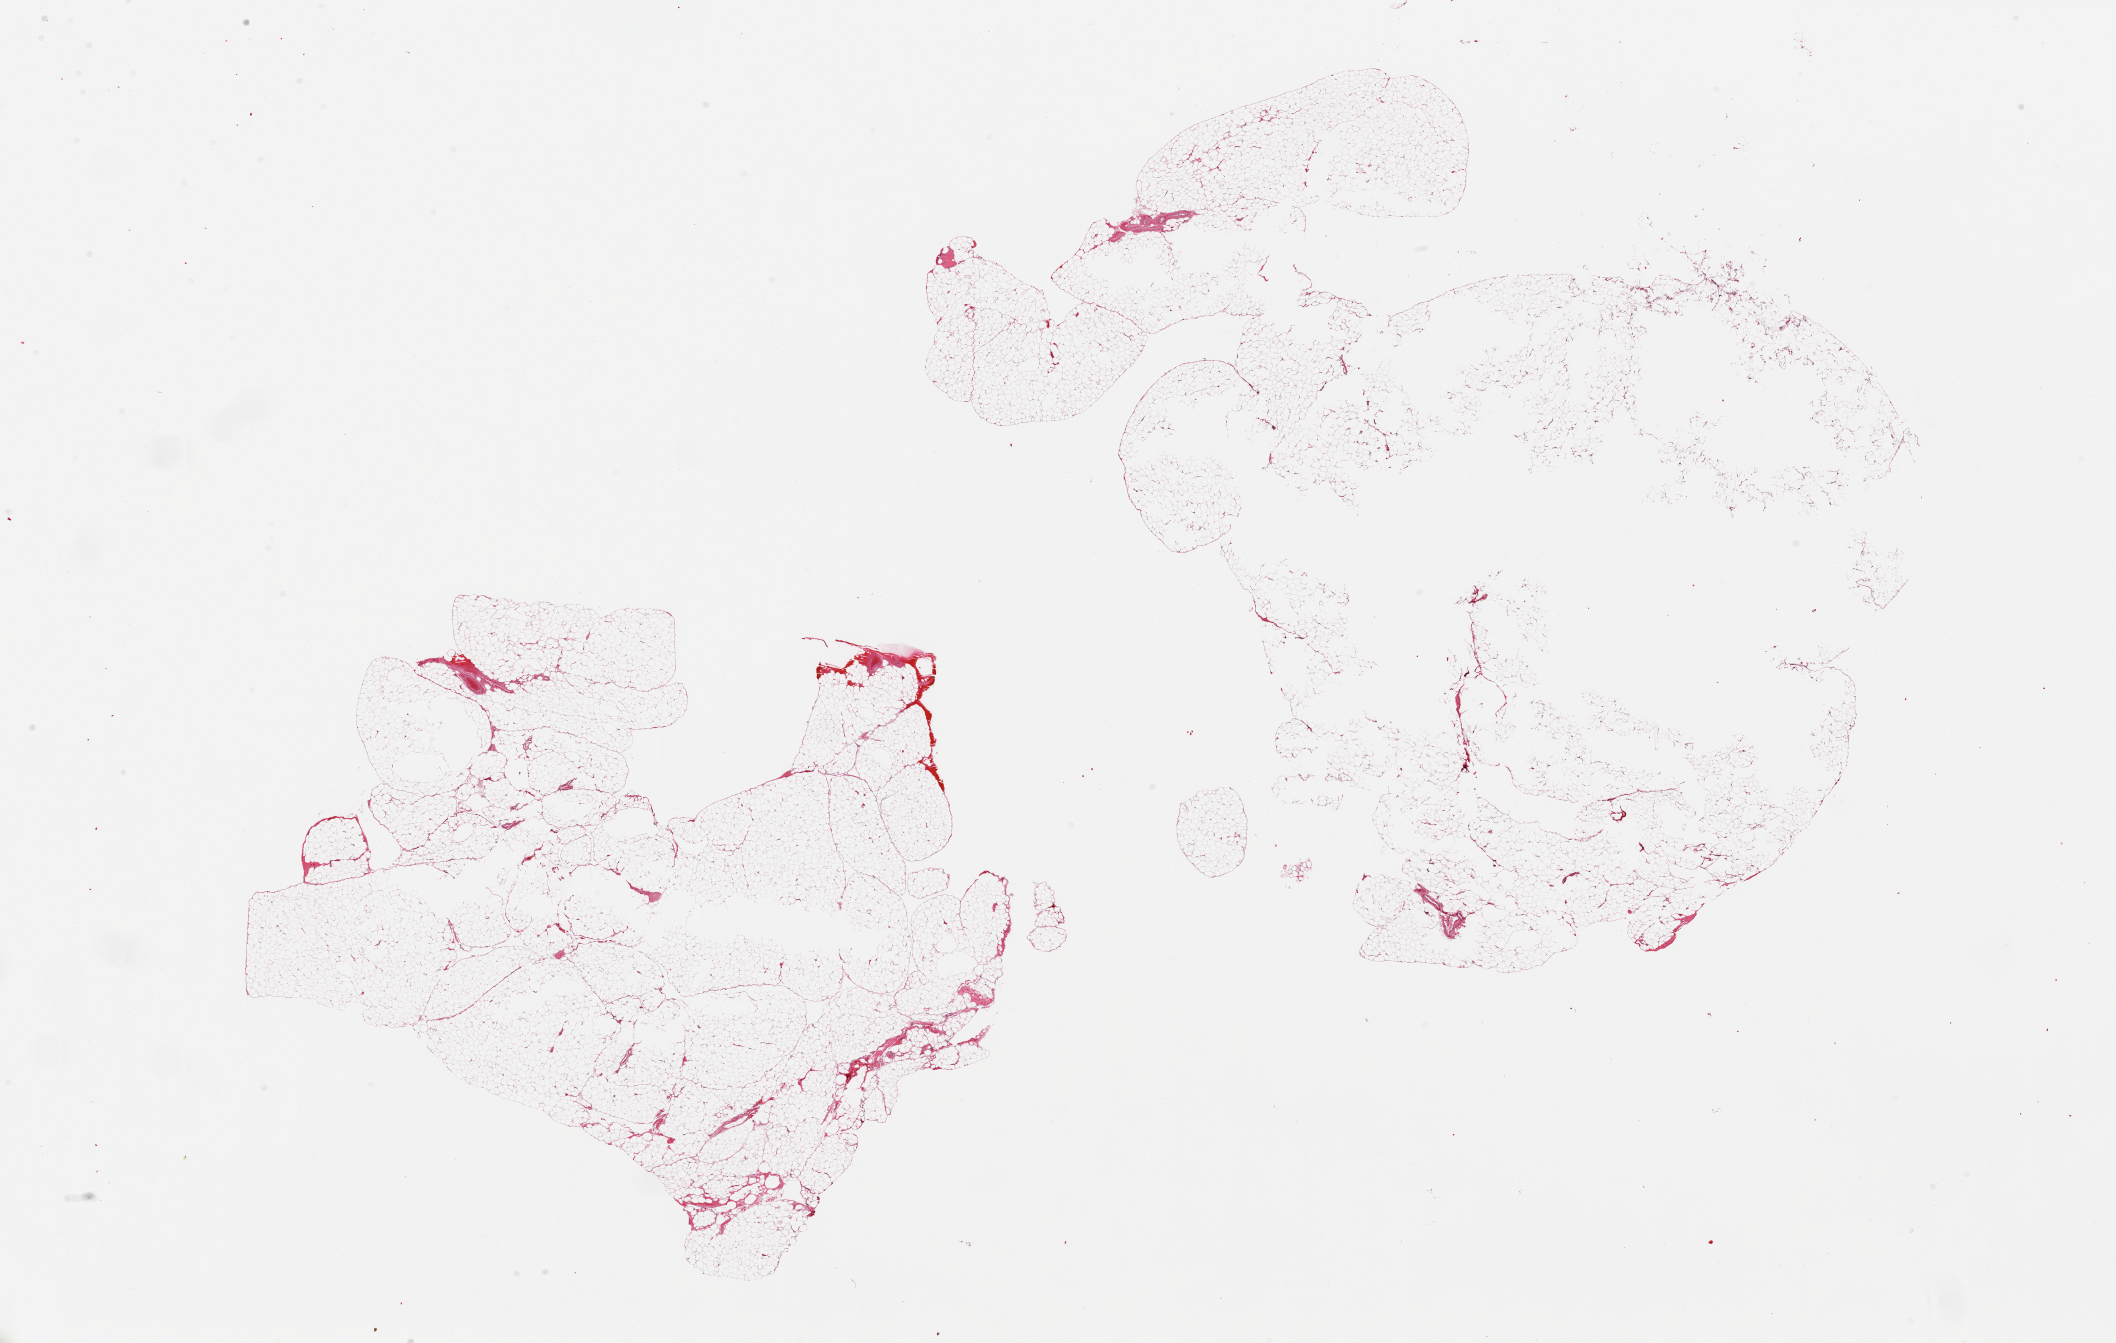
Whole-slide image, haematoxylin and eosin stain — low-resolution overview of the scanned area, about 33.5 x 21.2 mm (slide scanned at 20x); PAXgene-fixed, paraffin-embedded tissue; section of omentum (target tissue); donor tissue sample. Donor sex: male.
* pathologist's review note for this sample: 2 pieces; holes in tissue